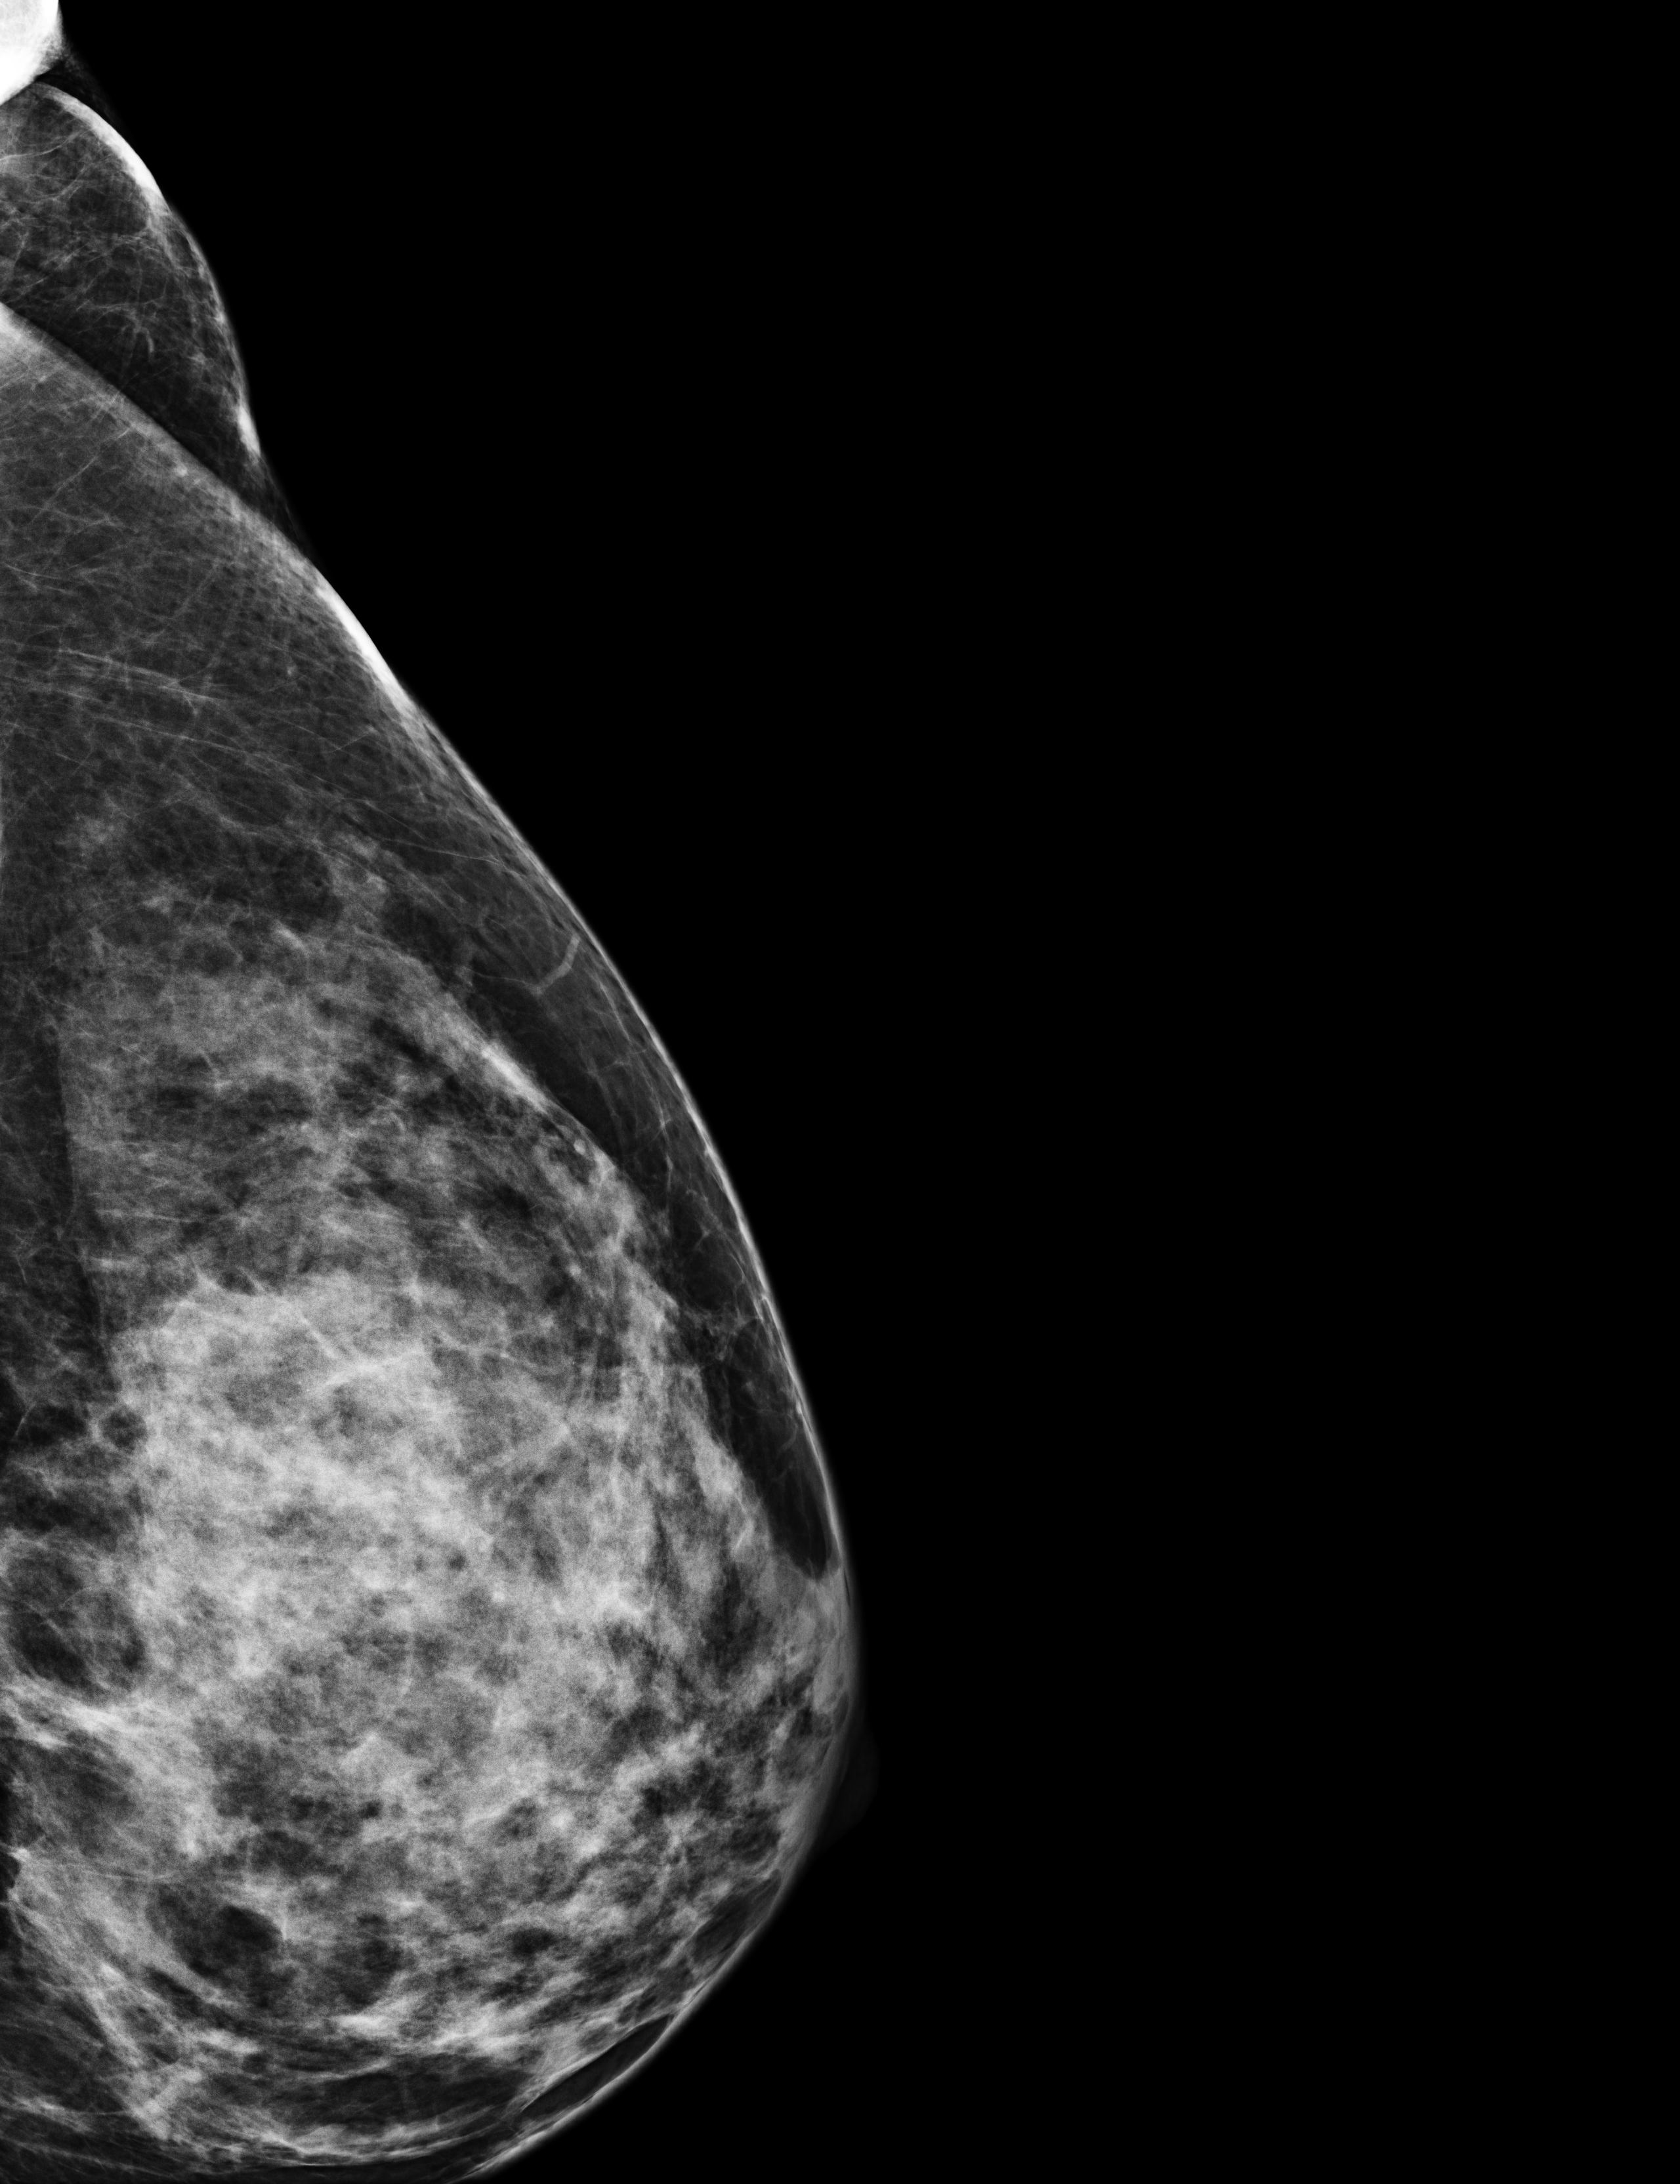
Full-field digital mammogram (FFDM); left breast; laterally exaggerated craniocaudal (XCCL) view; annual screening mammography examination; compressed breast thickness 55 mm. Patient aged 42 years (female).
Breast density at the screening exam (both breasts): extremely dense (BI-RADS density category d). Final BI-RADS category for the screening round (tomosynthesis exam, both breasts): category 1. Recall: no recall after this screen.